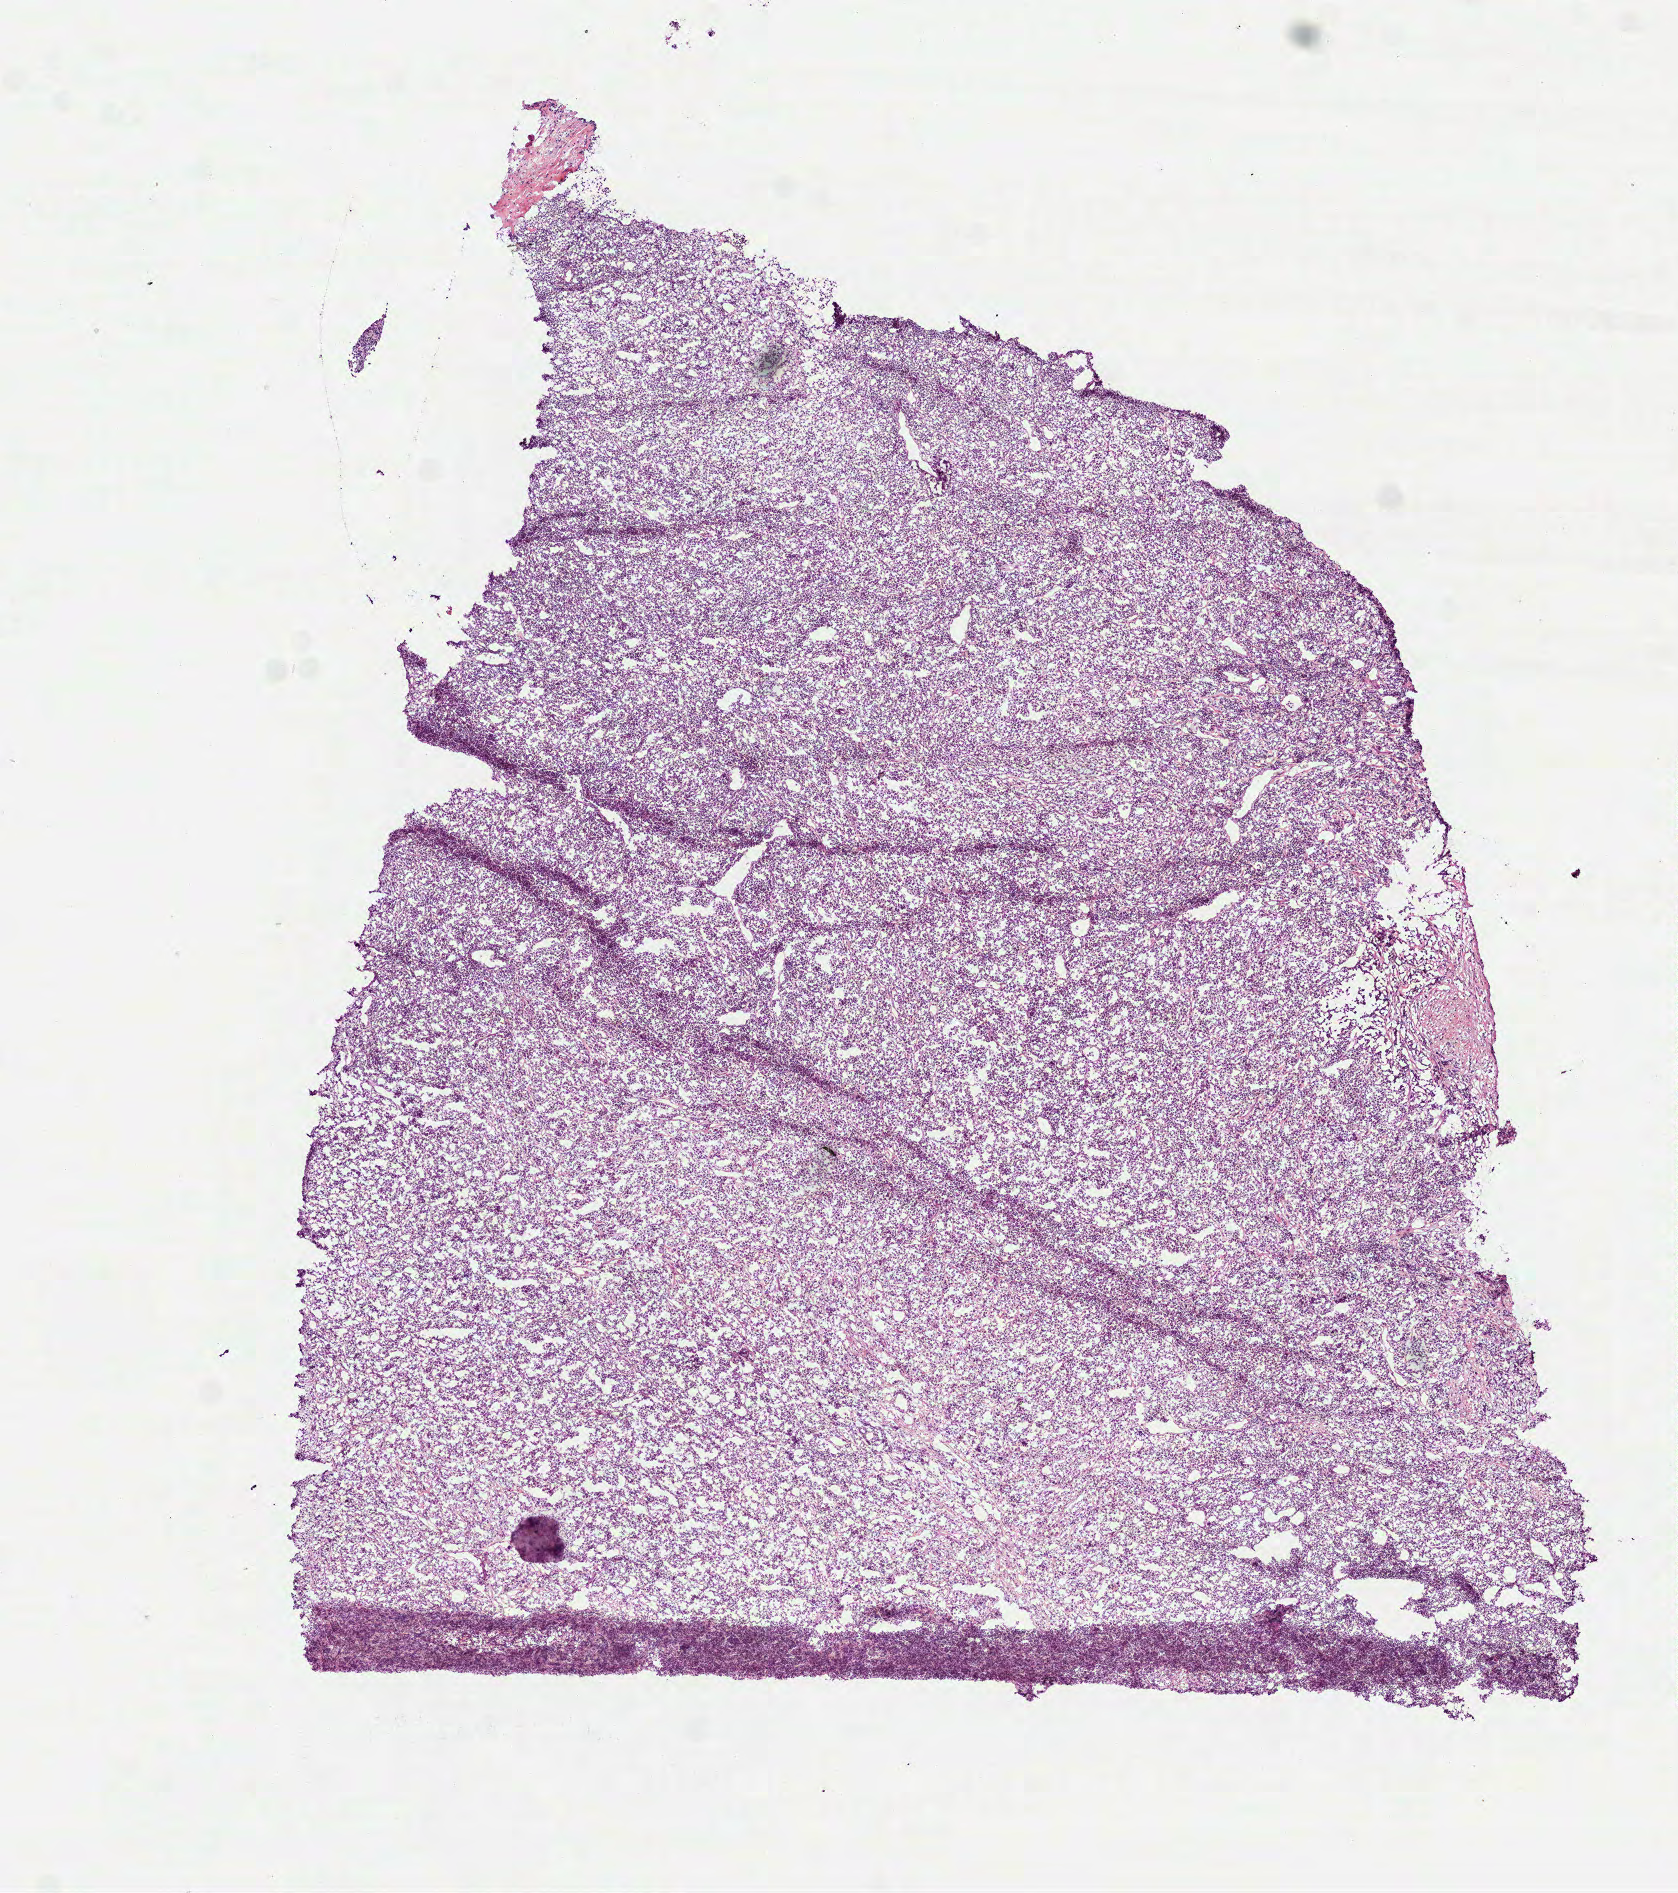
Hematoxylin and eosin (H&E) stained whole-slide image — low-resolution overview of the scanned area, about 6.8 x 7.6 mm (acquisition: 40x scan). Frozen section from the top of the tissue portion. Primary tumour sample from the lymphoid tissue. Patient: male, age at initial diagnosis 58 years. Slide review estimates, as recorded: tumour cells 100%, tumour nuclei 90%, normal cells 0%, stromal cells 0%, necrosis 0%. Inflammatory infiltration, as recorded: lymphocyte infiltration 90%, monocyte infiltration 0%, neutrophil infiltration 0%.
Histologic diagnosis: Diffuse large B-cell lymphoma, NOS.